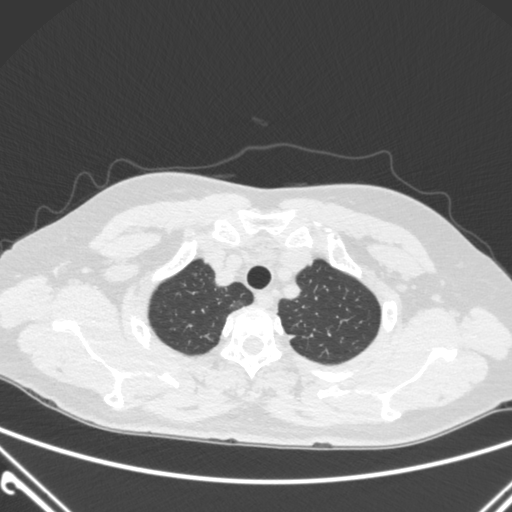
Chest CT, one axial slice. Position 248 of 300 along the scan axis. Lung window (W 1500 / L -600 HU). 512 × 512 image matrix, field of view 350 × 350 mm. Female patient, age 54 years. From the clinical record (not read from this slice): clinical TNM (as recorded): T1a N0 M0; histopathological grade: G1.
Outlined on this slice (rectangle marked by the reading radiologist):
- lung tumour (recorded histology: adenocarcinoma): bounding box (x1, y1, x2, y2) in pixels: (228, 296, 253, 313)